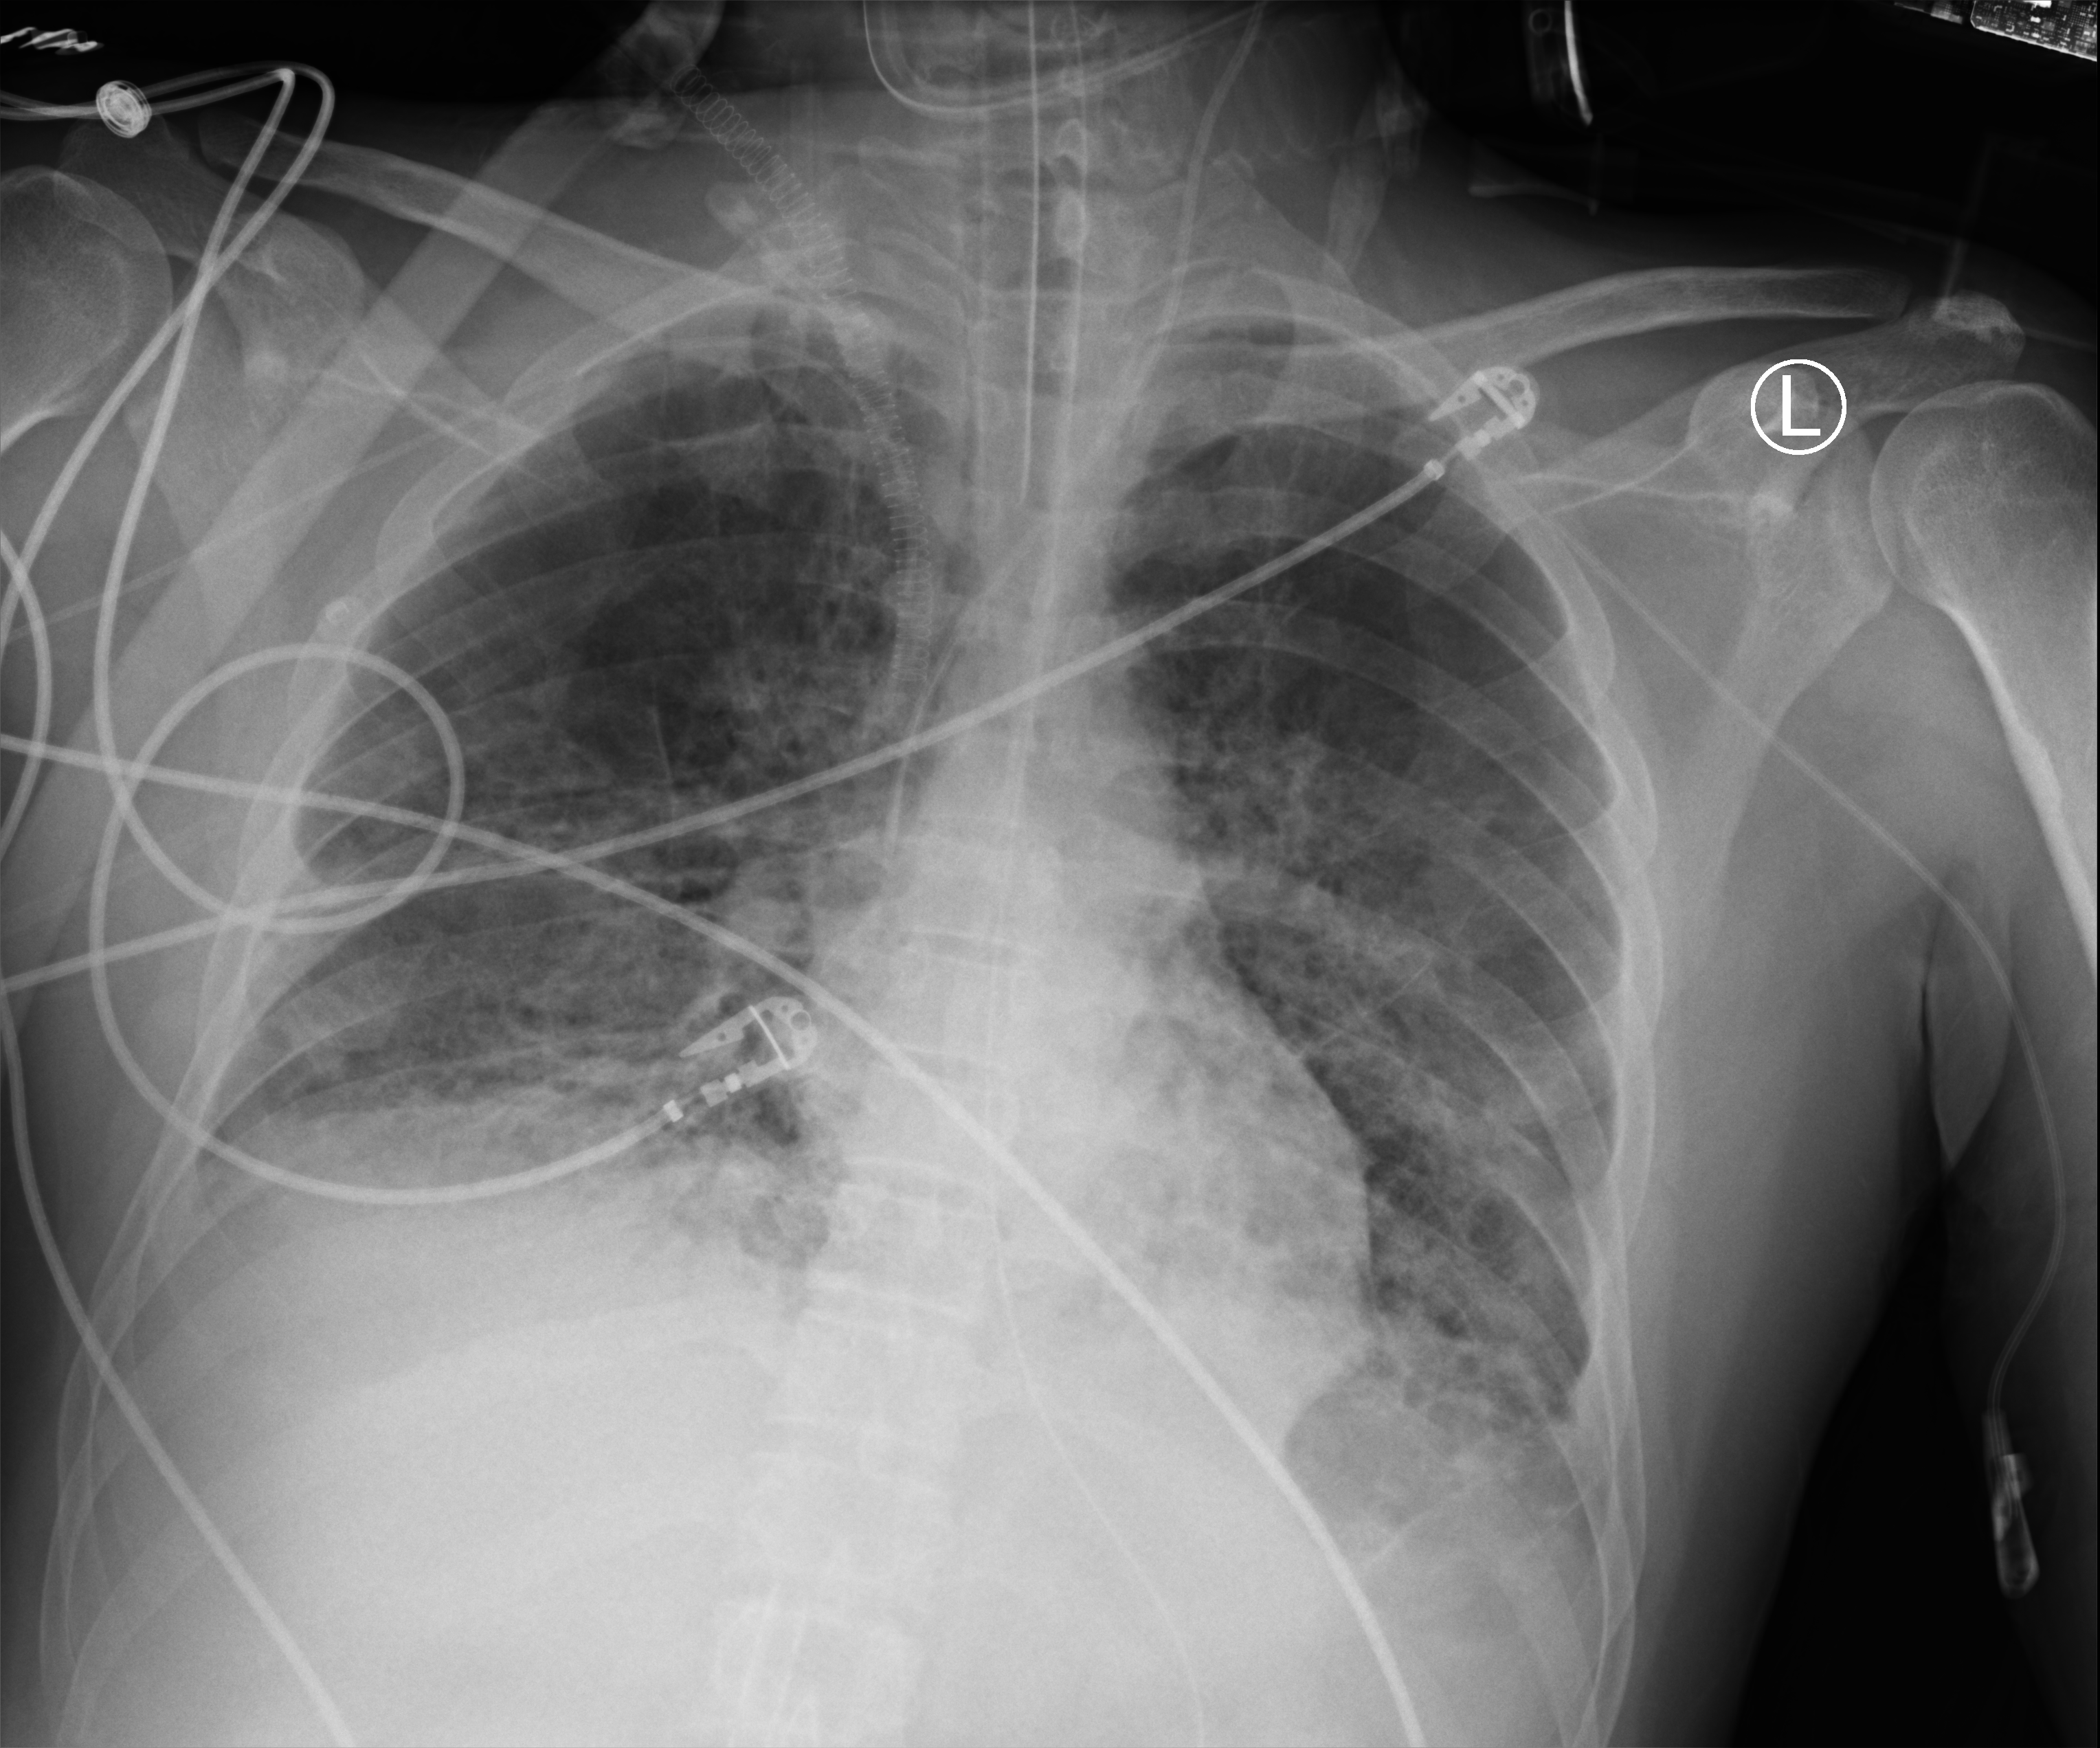
Bedside chest radiograph (computed radiography), anteroposterior (AP) projection. Adult patient hospitalised with COVID-19, age 18–59 years.
From the hospital-stay record, not from the radiograph (when in the stay this image was taken is not recorded): mechanically ventilated during this hospital stay: yes.